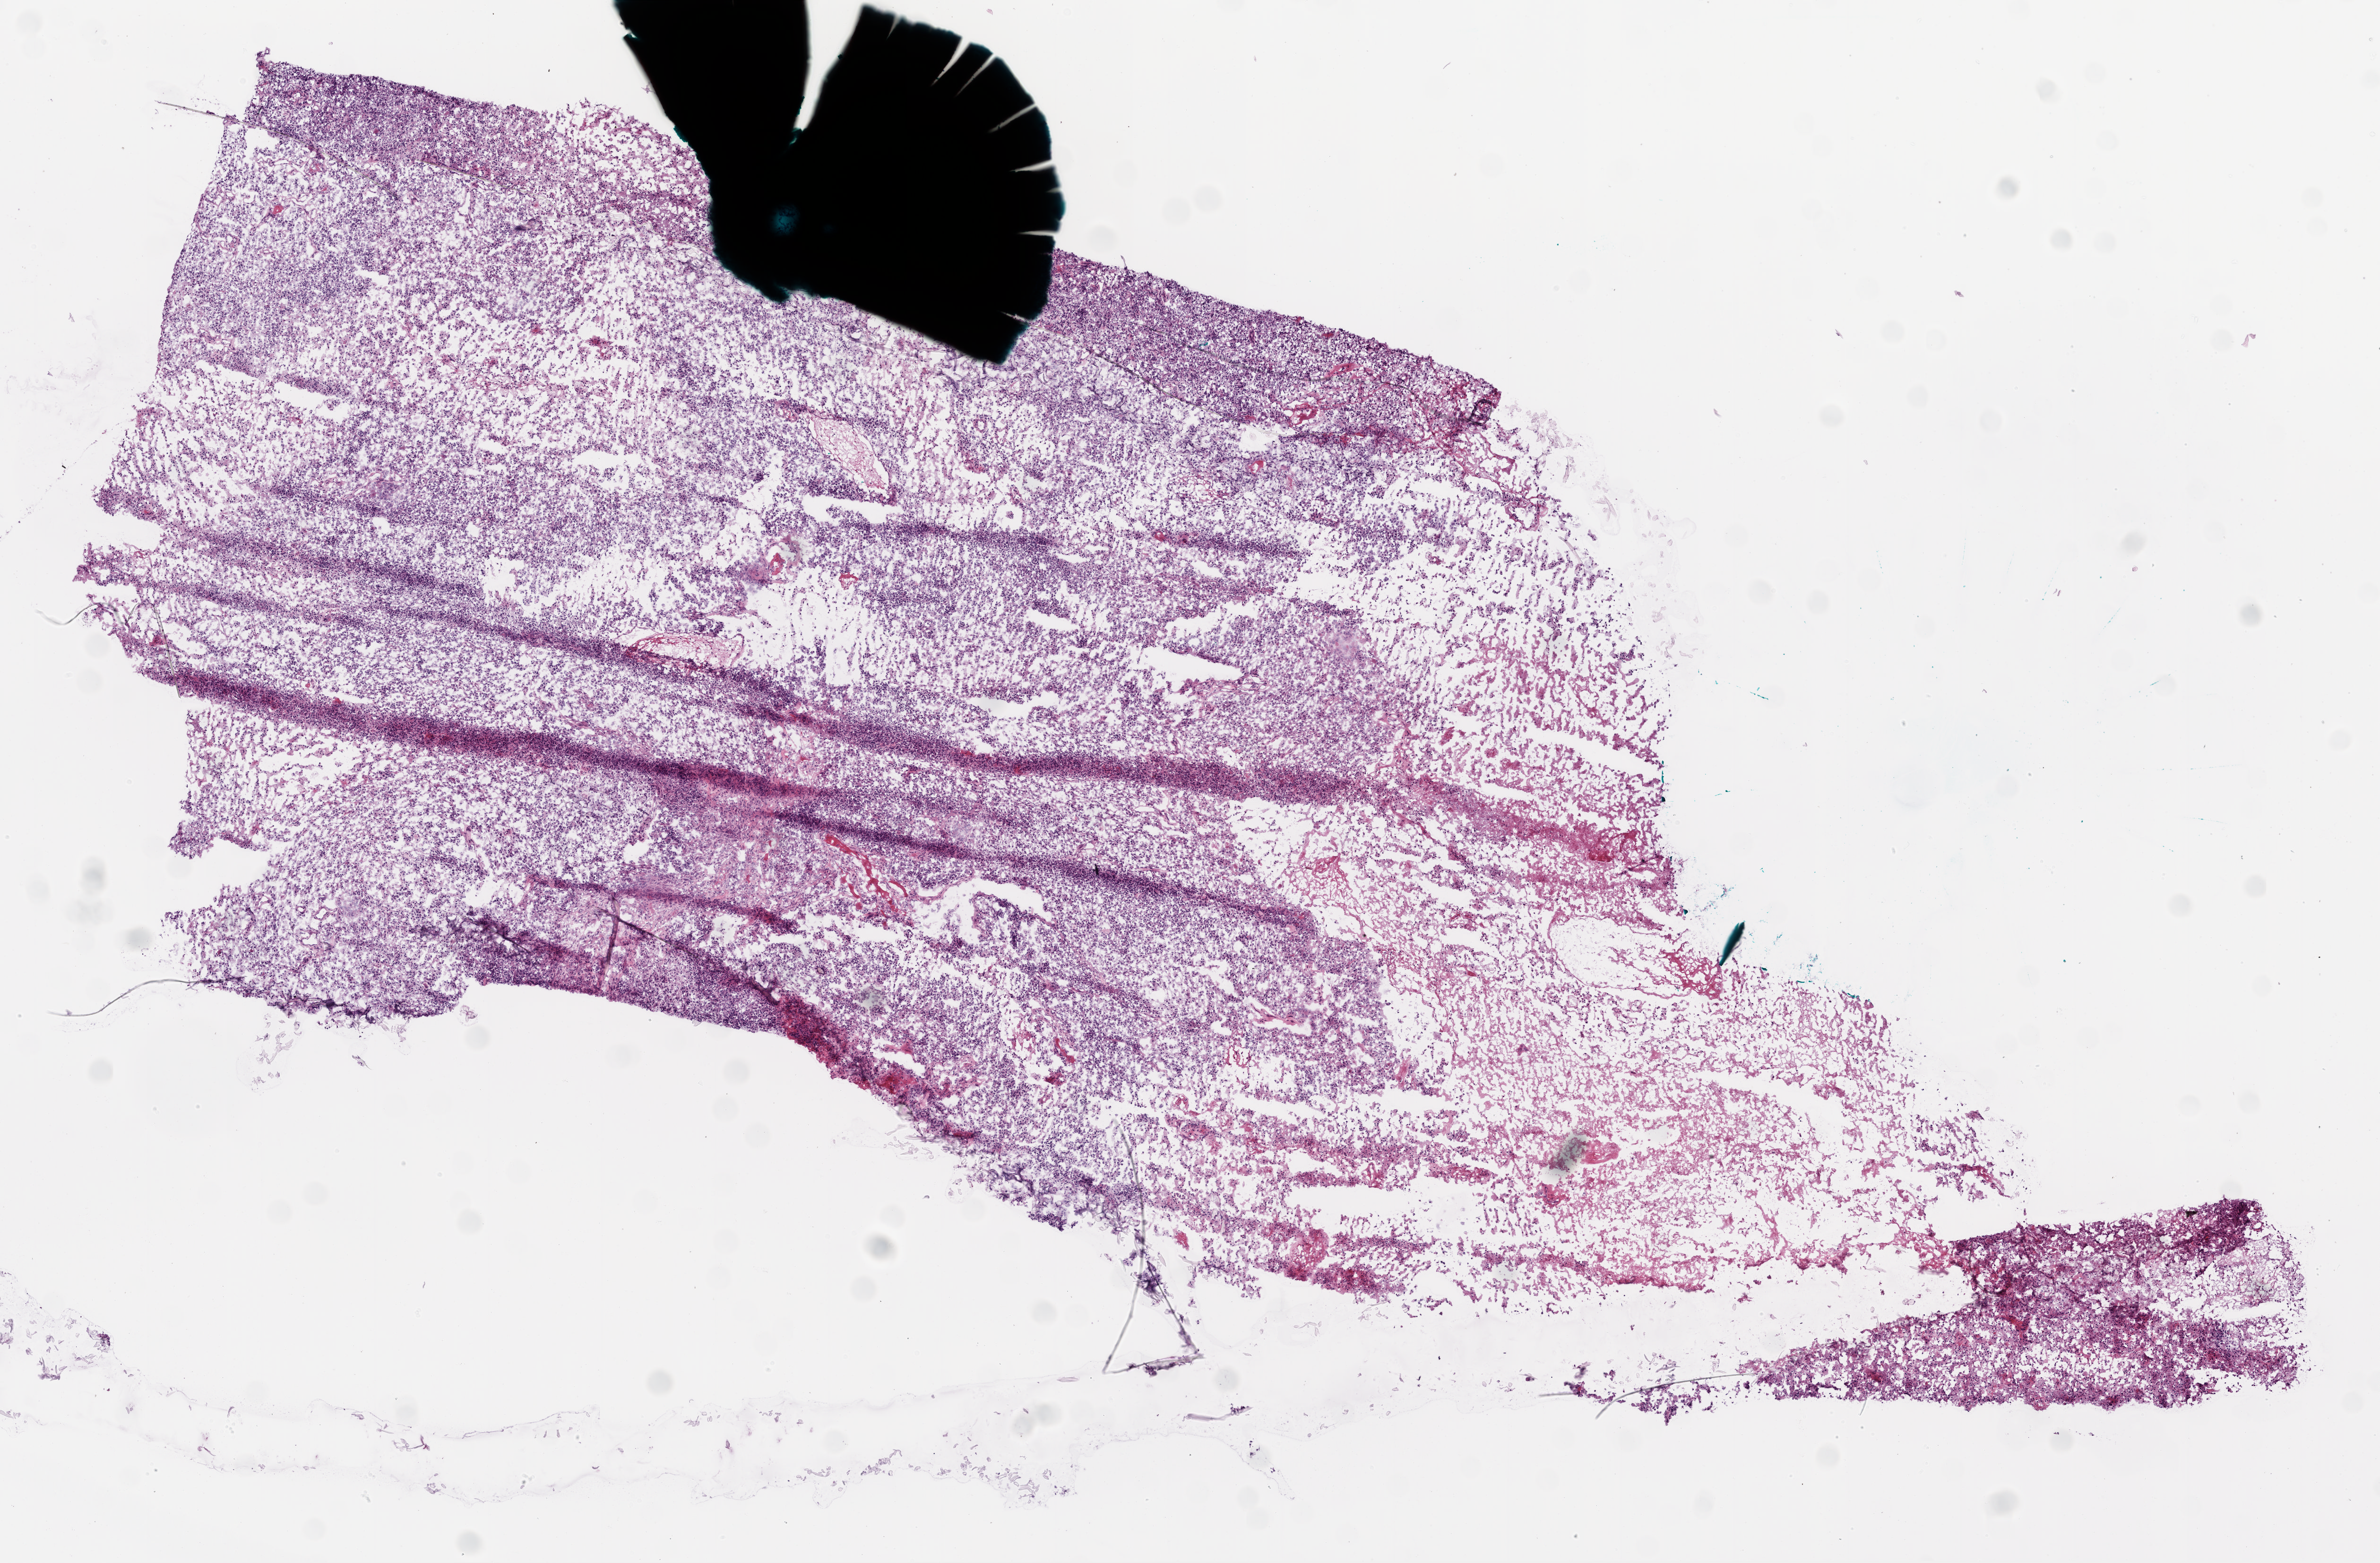
Whole-slide histology image, Hematoxylin and eosin (H&E) stained — low-resolution overview of the scanned area, about 10.2 x 6.7 mm; frozen section; sample: primary tumour, brain. Patient: female, age at initial diagnosis 57 years. Pathologist review of this section (percent, as recorded): tumour cells 75%, tumour nuclei 90%, normal cells 0%, stromal cells 0%, necrosis 25%. Infiltration values recorded for this section: lymphocyte infiltration 0%, neutrophil infiltration 0%.
• histologic diagnosis: Glioblastoma